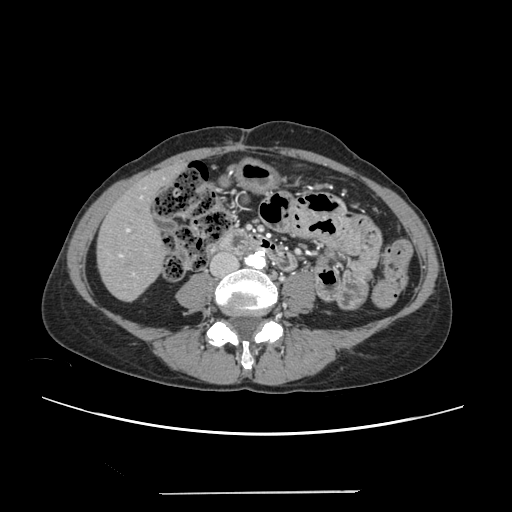
Contrast-enhanced abdominal CT, one axial slice. 120 kVp. Intravenous contrast given. Soft-tissue window (W 400 / L 40 HU). 1.25 mm slice thickness. 512 × 512 image matrix, field of view 371 × 371 mm. Female patient, age 60 years. From the clinical record (not read from this slice): diagnosis: colorectal cancer liver metastases, imaged before liver resection; multiple liver metastases: no; largest metastasis: 1.5 cm; disease in both lobes: no.
Outlined on this slice (expert manual segmentation):
- liver: box from (x=98, y=168) to (x=178, y=300) px
- planned liver remnant (the part of the liver to remain after resection): (x=98, y=171)–(x=170, y=300)
- portal vein (with intrahepatic branches): (x=119, y=187)–(x=146, y=276)